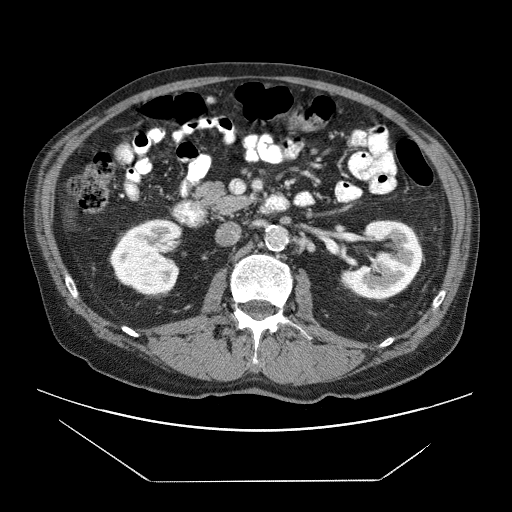
Contrast-enhanced abdominal CT (liver protocol), one axial slice. Slice 8 of 83 in the series (ordered by position). 120 kVp. Soft-tissue window (W 400 / L 40 HU). 2.5 mm slice thickness. 512 × 512 image matrix, field of view 420 × 420 mm. From the clinical record (not read from this slice): diagnosis: hepatocellular carcinoma (patient treated with transarterial chemoembolisation; whether this scan precedes or follows treatment is not stated here); TNM stage (as recorded): Stage-IVB; Child-Pugh class: B; tumour differentiation: poorly differentiated; tumour nodularity: uninodular.
Structures marked on this image (semi-automatically segmented with operator editing):
- liver parenchyma outside the tumour (the mass and vessels are separate outlines, so this box may not span the whole liver): bounding box [x1, y1, x2, y2] px = [66, 215, 70, 221]